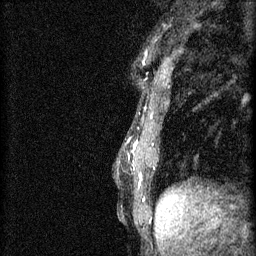
Breast MRI (dynamic contrast-enhanced), one sagittal slice. 3 images stored at this slice position (order not interpretable as contrast timing). 1.5 T. TE 4.2 ms, TR 11 ms. 2 mm slice thickness. 256 × 256 image matrix, field of view 180 × 180 mm. Patient: female, 37 years.
Annotated regions visible in this slice (semi-automatic segmentation, software-assisted and operator-edited):
- analysis volume of interest (the breast-tissue region the enhancement analysis was run in; not a lesion): bounding box (x1, y1, x2, y2) in pixels: (128, 142, 156, 167)
- tumour enhancement mask (voxels above the 70 % enhancement threshold inside the analysis volume of interest): (128, 142, 137, 159)